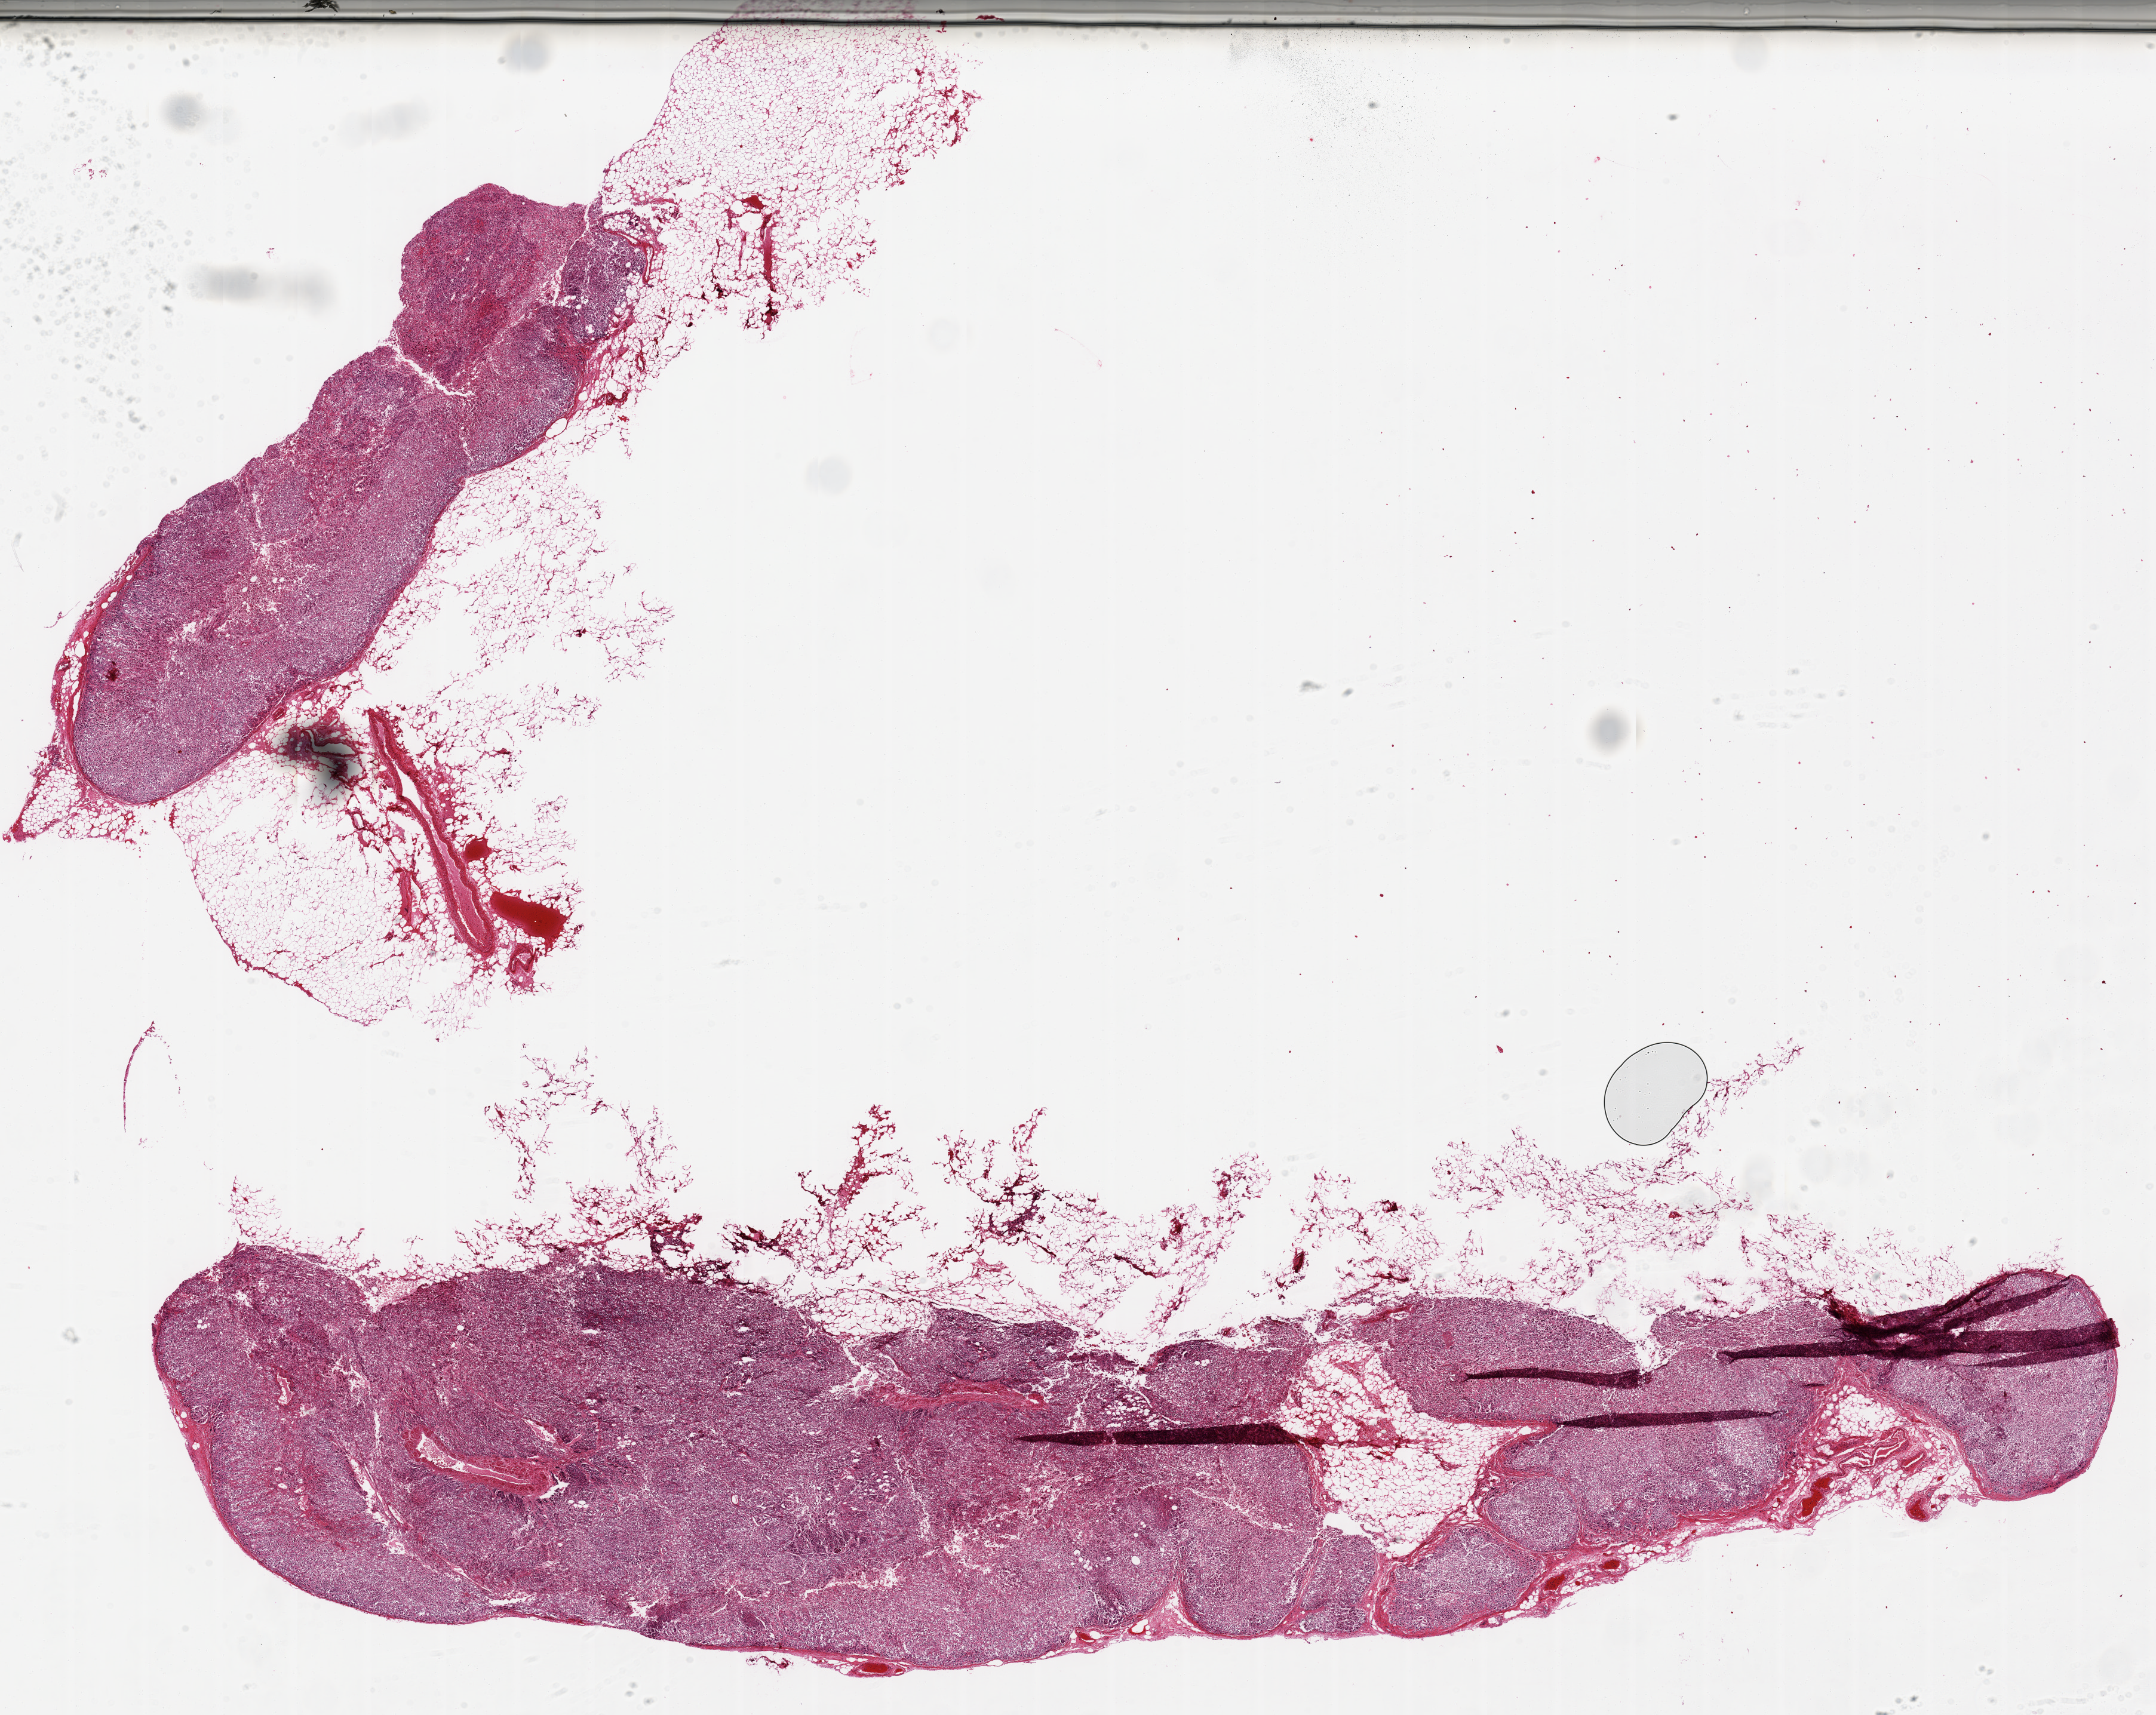
H&E whole-slide image — shown as a low-resolution overview of the whole scanned area (about 28.5 x 22.7 mm); PAXgene-fixed, paraffin-embedded tissue; section of adrenal gland (target tissue); tissue donor sample.
• reviewer comment on this tissue sample: Two pieces: 26x5mm, 10x3mm